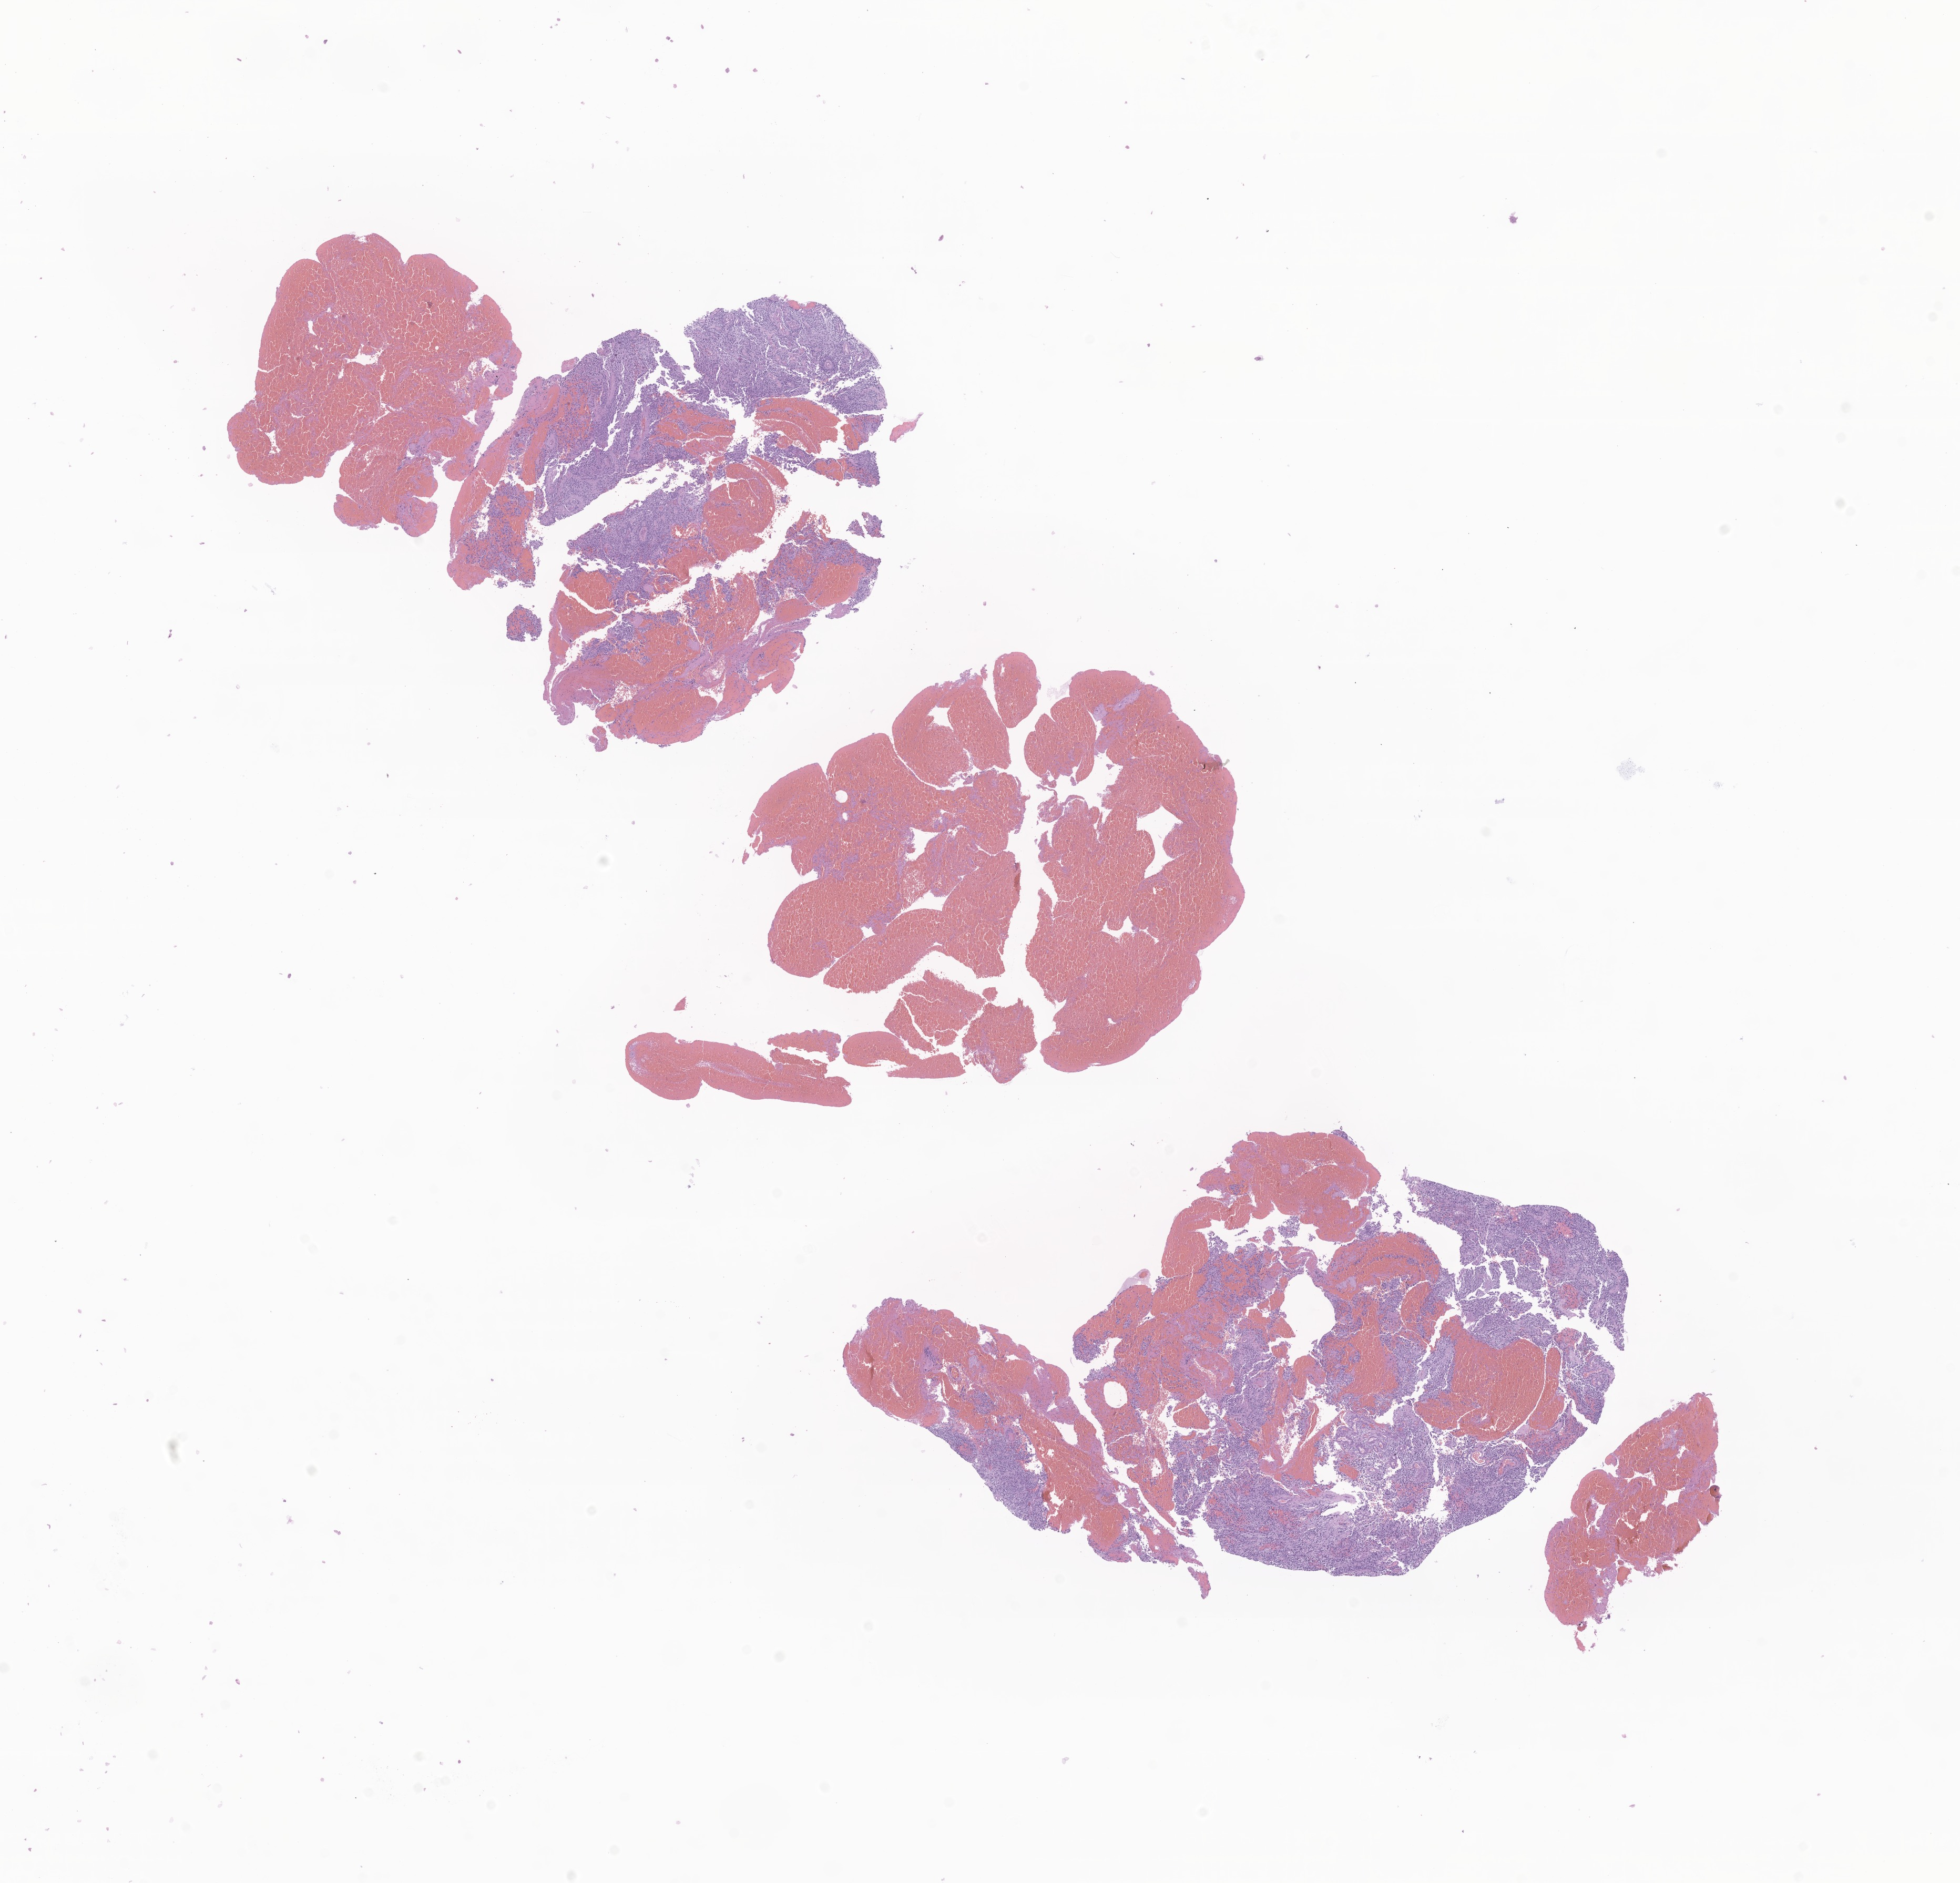
Whole-slide image, haematoxylin and eosin stain of tumor tissue from the brain — a low-resolution overview of the entire scanned area, about 15.7 x 15.1 mm; formalin-fixed, paraffin-embedded (FFPE) tissue. Female patient, age 205 months.
* diagnosis: Glioma, malignant